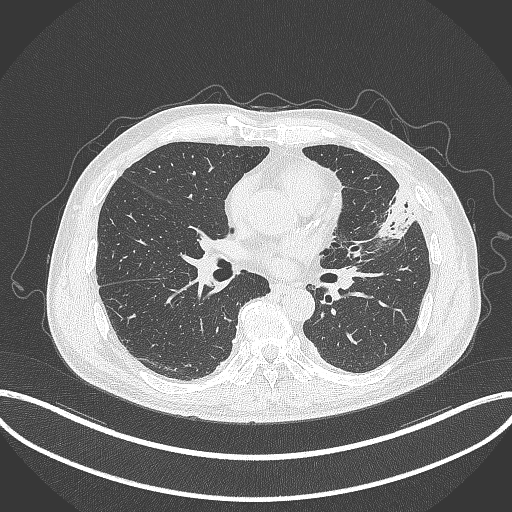
Chest CT, one axial slice. Position 162 of 382 along the scan axis. 120 kVp. Lung window (W 1500 / L -600 HU). 1 mm slice thickness. 512 × 512 image matrix, field of view 415 × 415 mm. Male patient, age 64 years. From the clinical record (not read from this slice): clinical TNM (as recorded): T4 N1 M0; histopathological grade: G3.
Outlined on this slice (bounding box drawn by a radiologist):
- lung tumour (recorded histology: adenocarcinoma): bounding box [x1, y1, x2, y2] px = [376, 187, 419, 243]